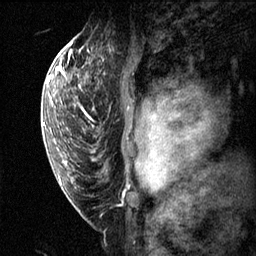
Breast MRI (dynamic contrast-enhanced), one sagittal slice. Slice 43 of 60 in the series (ordered by position). Dynamic contrast-enhanced series, image 2 of 3 at this slice position (ordered by acquisition). 1.5 T. TE 4.2 ms, TR 11.1 ms. 256 × 256 image matrix, field of view 180 × 180 mm. Female patient, age 50 years.
Structures marked on this image (semi-automatic segmentation, software-assisted and operator-edited):
- analysis volume of interest (the breast-tissue region the enhancement analysis was run in; not a lesion): bounding box <82,60,161,143> (left, top, right, bottom; pixels)
- tumour enhancement mask (voxels above the 70 % enhancement threshold inside the analysis volume of interest): <127,108,161,131>